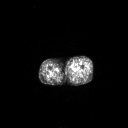
FDG PET of an extremity soft-tissue mass (from a PET/CT study), one axial slice; position 236 of 267 along the scan axis; 3.27 mm slice thickness; 128 × 128 image matrix, field of view 700 × 700 mm. Patient: male, 48 years. Case-level facts recorded for this patient, not image findings: histological type: pleiomorphic leiomyosarcoma; grade: high; site of the primary tumour: left thigh.
Structures marked on this image (expert contour drawn on MRI and transferred to this co-registered scan by the dataset authors):
- gross tumour volume including surrounding oedema: bounding box [x1, y1, x2, y2] px = [70, 65, 73, 69]